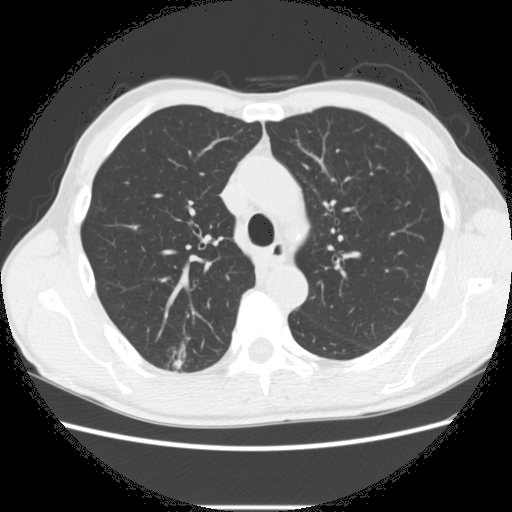
Low-dose screening chest CT, one axial slice. Reconstruction kernel STANDARD. Lung window (W 1500 / L -600 HU). 2.5 mm slice thickness. 512 × 512 image matrix.
Outlined on this slice (manually delineated by an expert):
- lesion 1 (tumor, upper lobe of right lung): bounding box <173,359,184,370> (left, top, right, bottom; pixels)